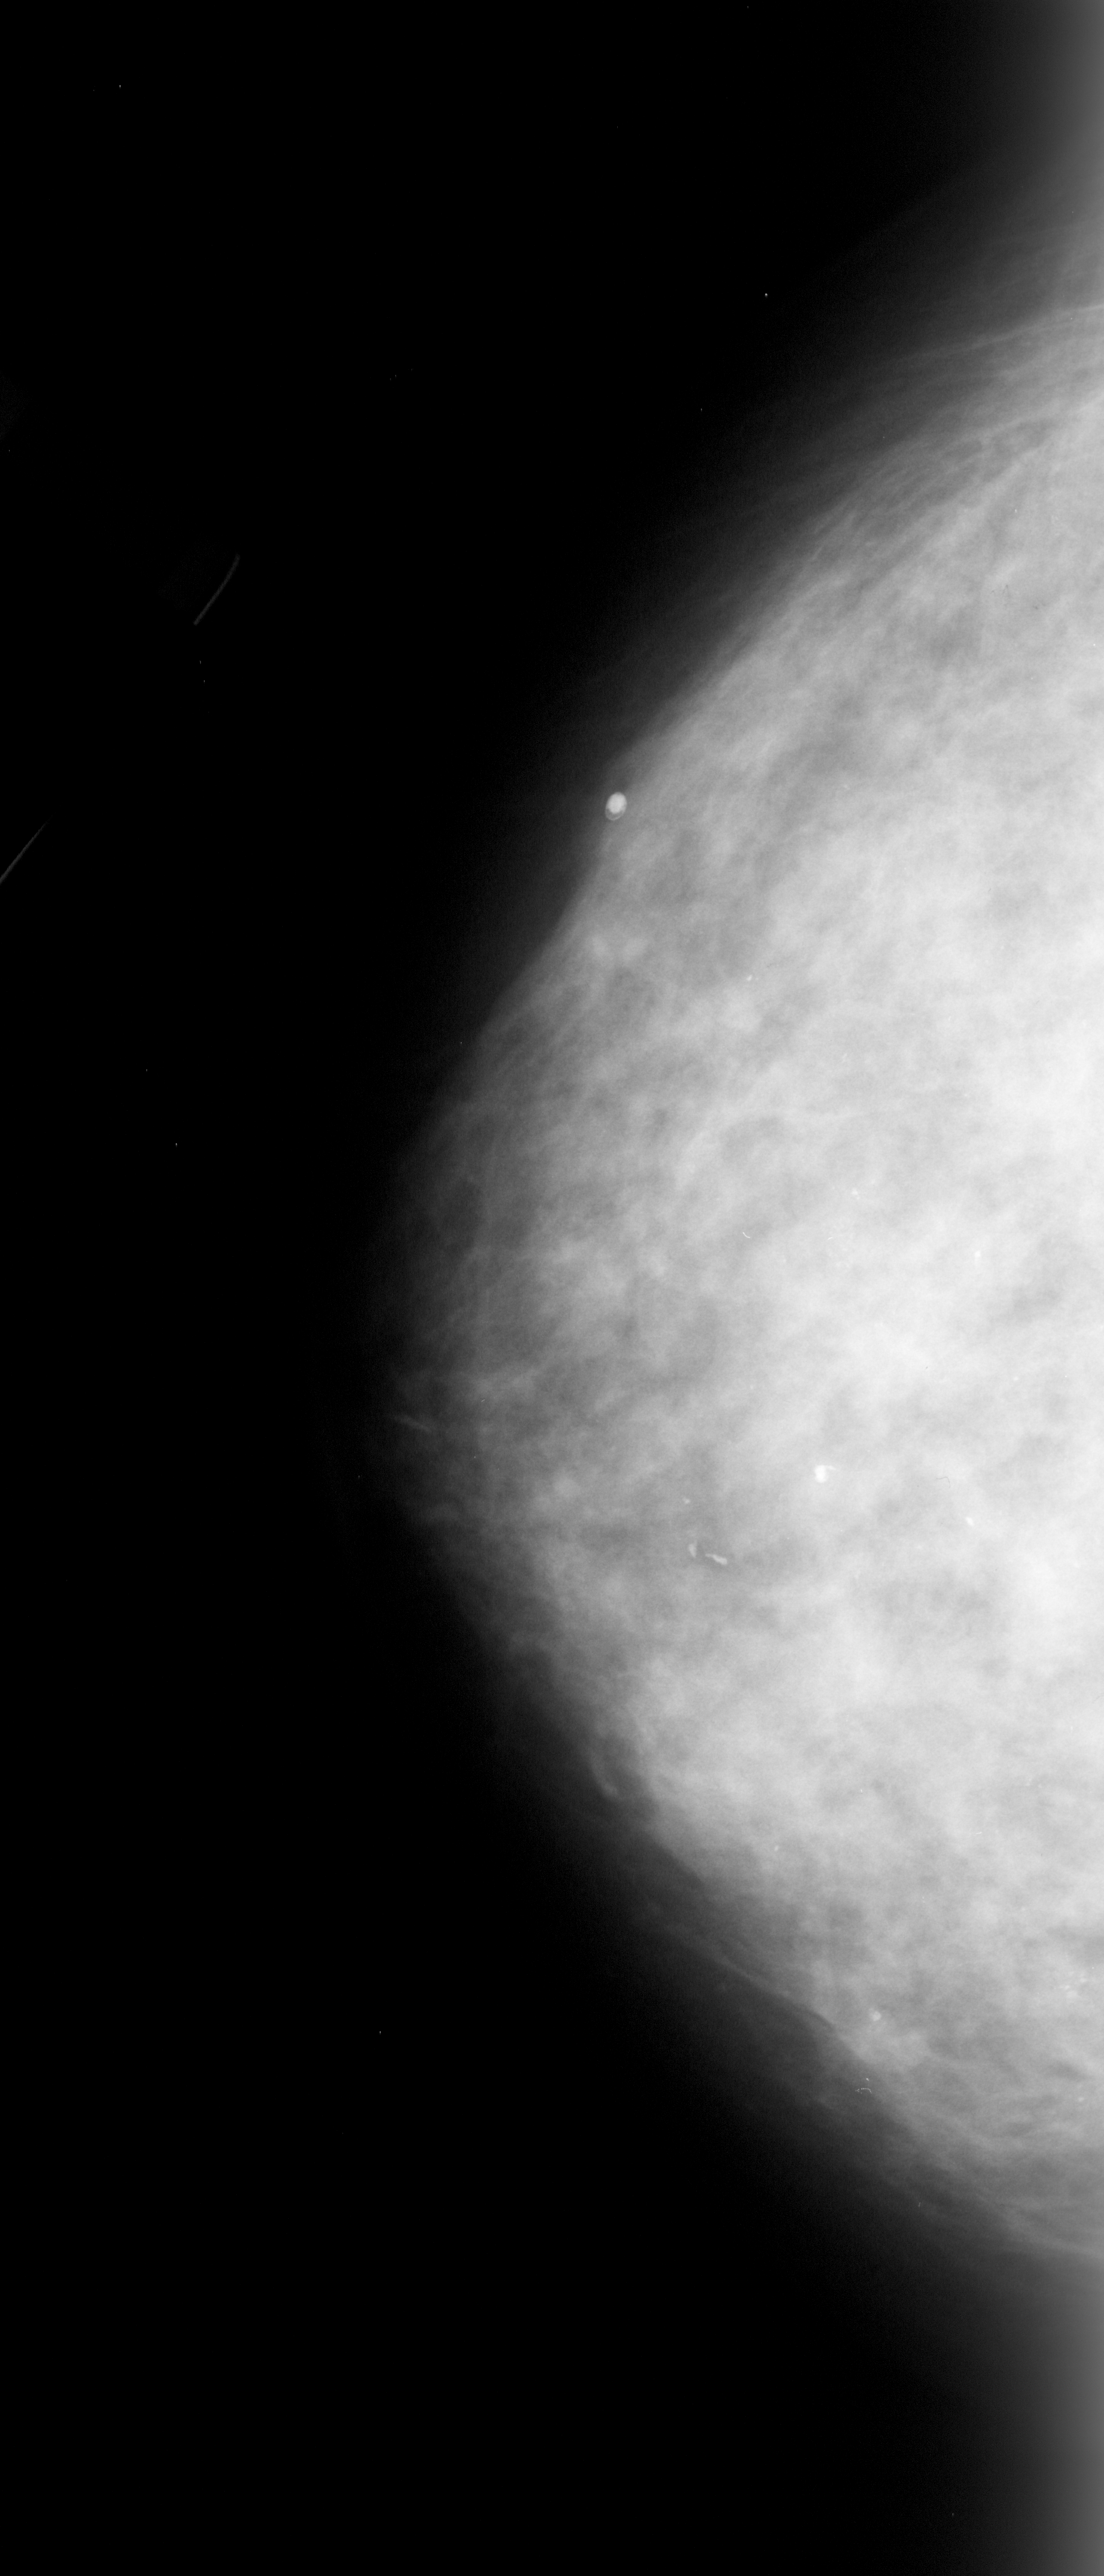
Digitized screen-film mammogram. Left breast. Craniocaudal (CC) view. Breast composition: heterogeneously dense (BI-RADS density category 3 of 4). 1104 × 2576 image matrix.
Expert-marked regions of interest on this image (one box per marked abnormality):
- calcifications, morphology pleomorphic, distribution segmental; BI-RADS assessment category 4; subtlety rating 3 on a 1 (subtle) to 5 (obvious) scale; pathology result (as recorded, not read from the image): malignant: box from (x=539, y=1128) to (x=1104, y=2147) px